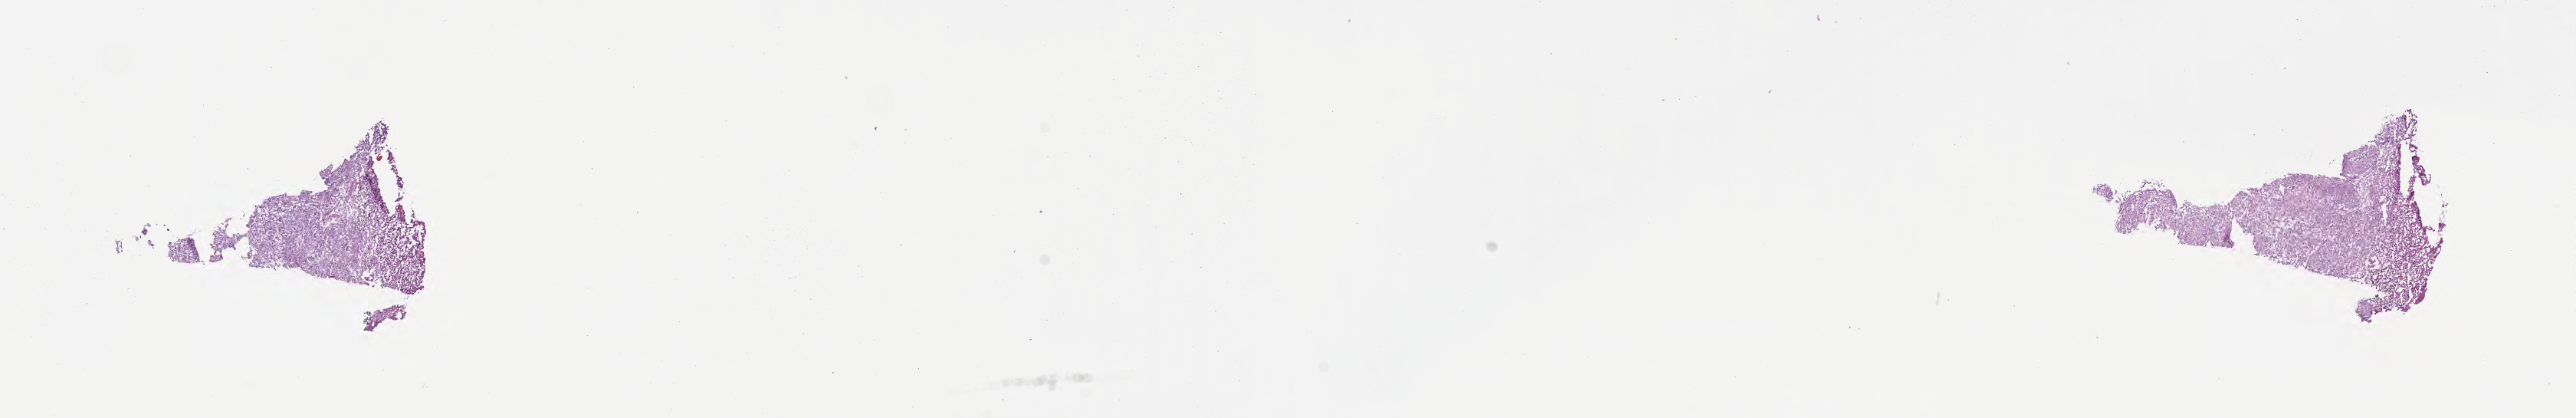
Digitized haematoxylin and eosin-stained section of tumor tissue from the brain, whole scanned area (about 27.2 x 4.4 mm) shown as a low-resolution overview; frozen section (OCT-embedded). Patient: female, age 225 months (18 years 9 months).
Diagnosis: Meningioma, NOS.